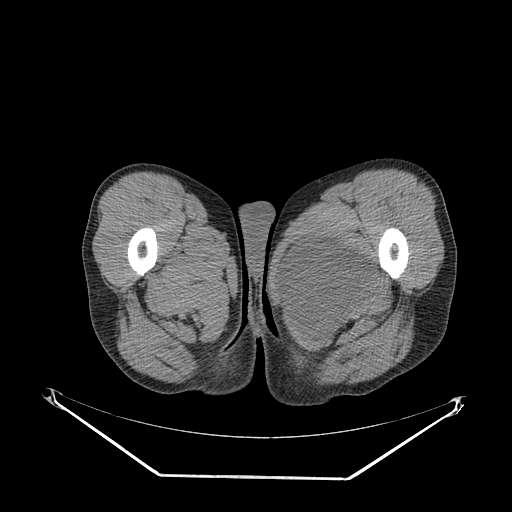
CT of an extremity soft-tissue mass (from a PET/CT study), one axial slice. Soft-tissue window (W 400 / L 40 HU). 512 × 512 image matrix, field of view 500 × 500 mm. Male patient. Case-level facts recorded for this patient, not image findings: histological type: pleiomorphic liposarcoma; grade: high; site of the primary tumour: left thigh.
Outlined on this slice (expert contour drawn on MRI and transferred to this co-registered scan by the dataset authors):
- gross tumour volume including surrounding oedema: bounding box [x1, y1, x2, y2] px = [283, 233, 371, 327]
- gross tumour volume (mass): [283, 235, 369, 318]